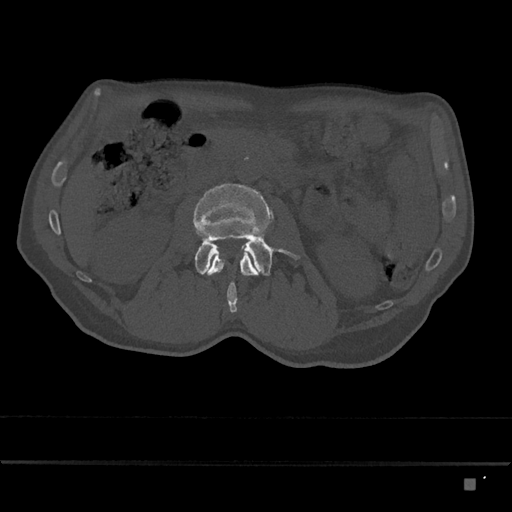
CT including the spine, one axial slice. Slice 434 of 797 in the series (ordered by position). Reconstruction kernel Br40s/3. 120 kVp. Bone window (W 1800 / L 400 HU). 0.5 mm slice thickness. 512 × 512 image matrix, field of view 390 × 390 mm. Patient: male, 72 years. From the clinical record (not read from this slice): primary cancer: prostate.
Structures marked on this image (semi-automatic segmentation, software-assisted and operator-edited):
- L2 vertebra: bounding box <205,250,259,313> (left, top, right, bottom; pixels)
- L3 vertebra: <193,183,300,276>